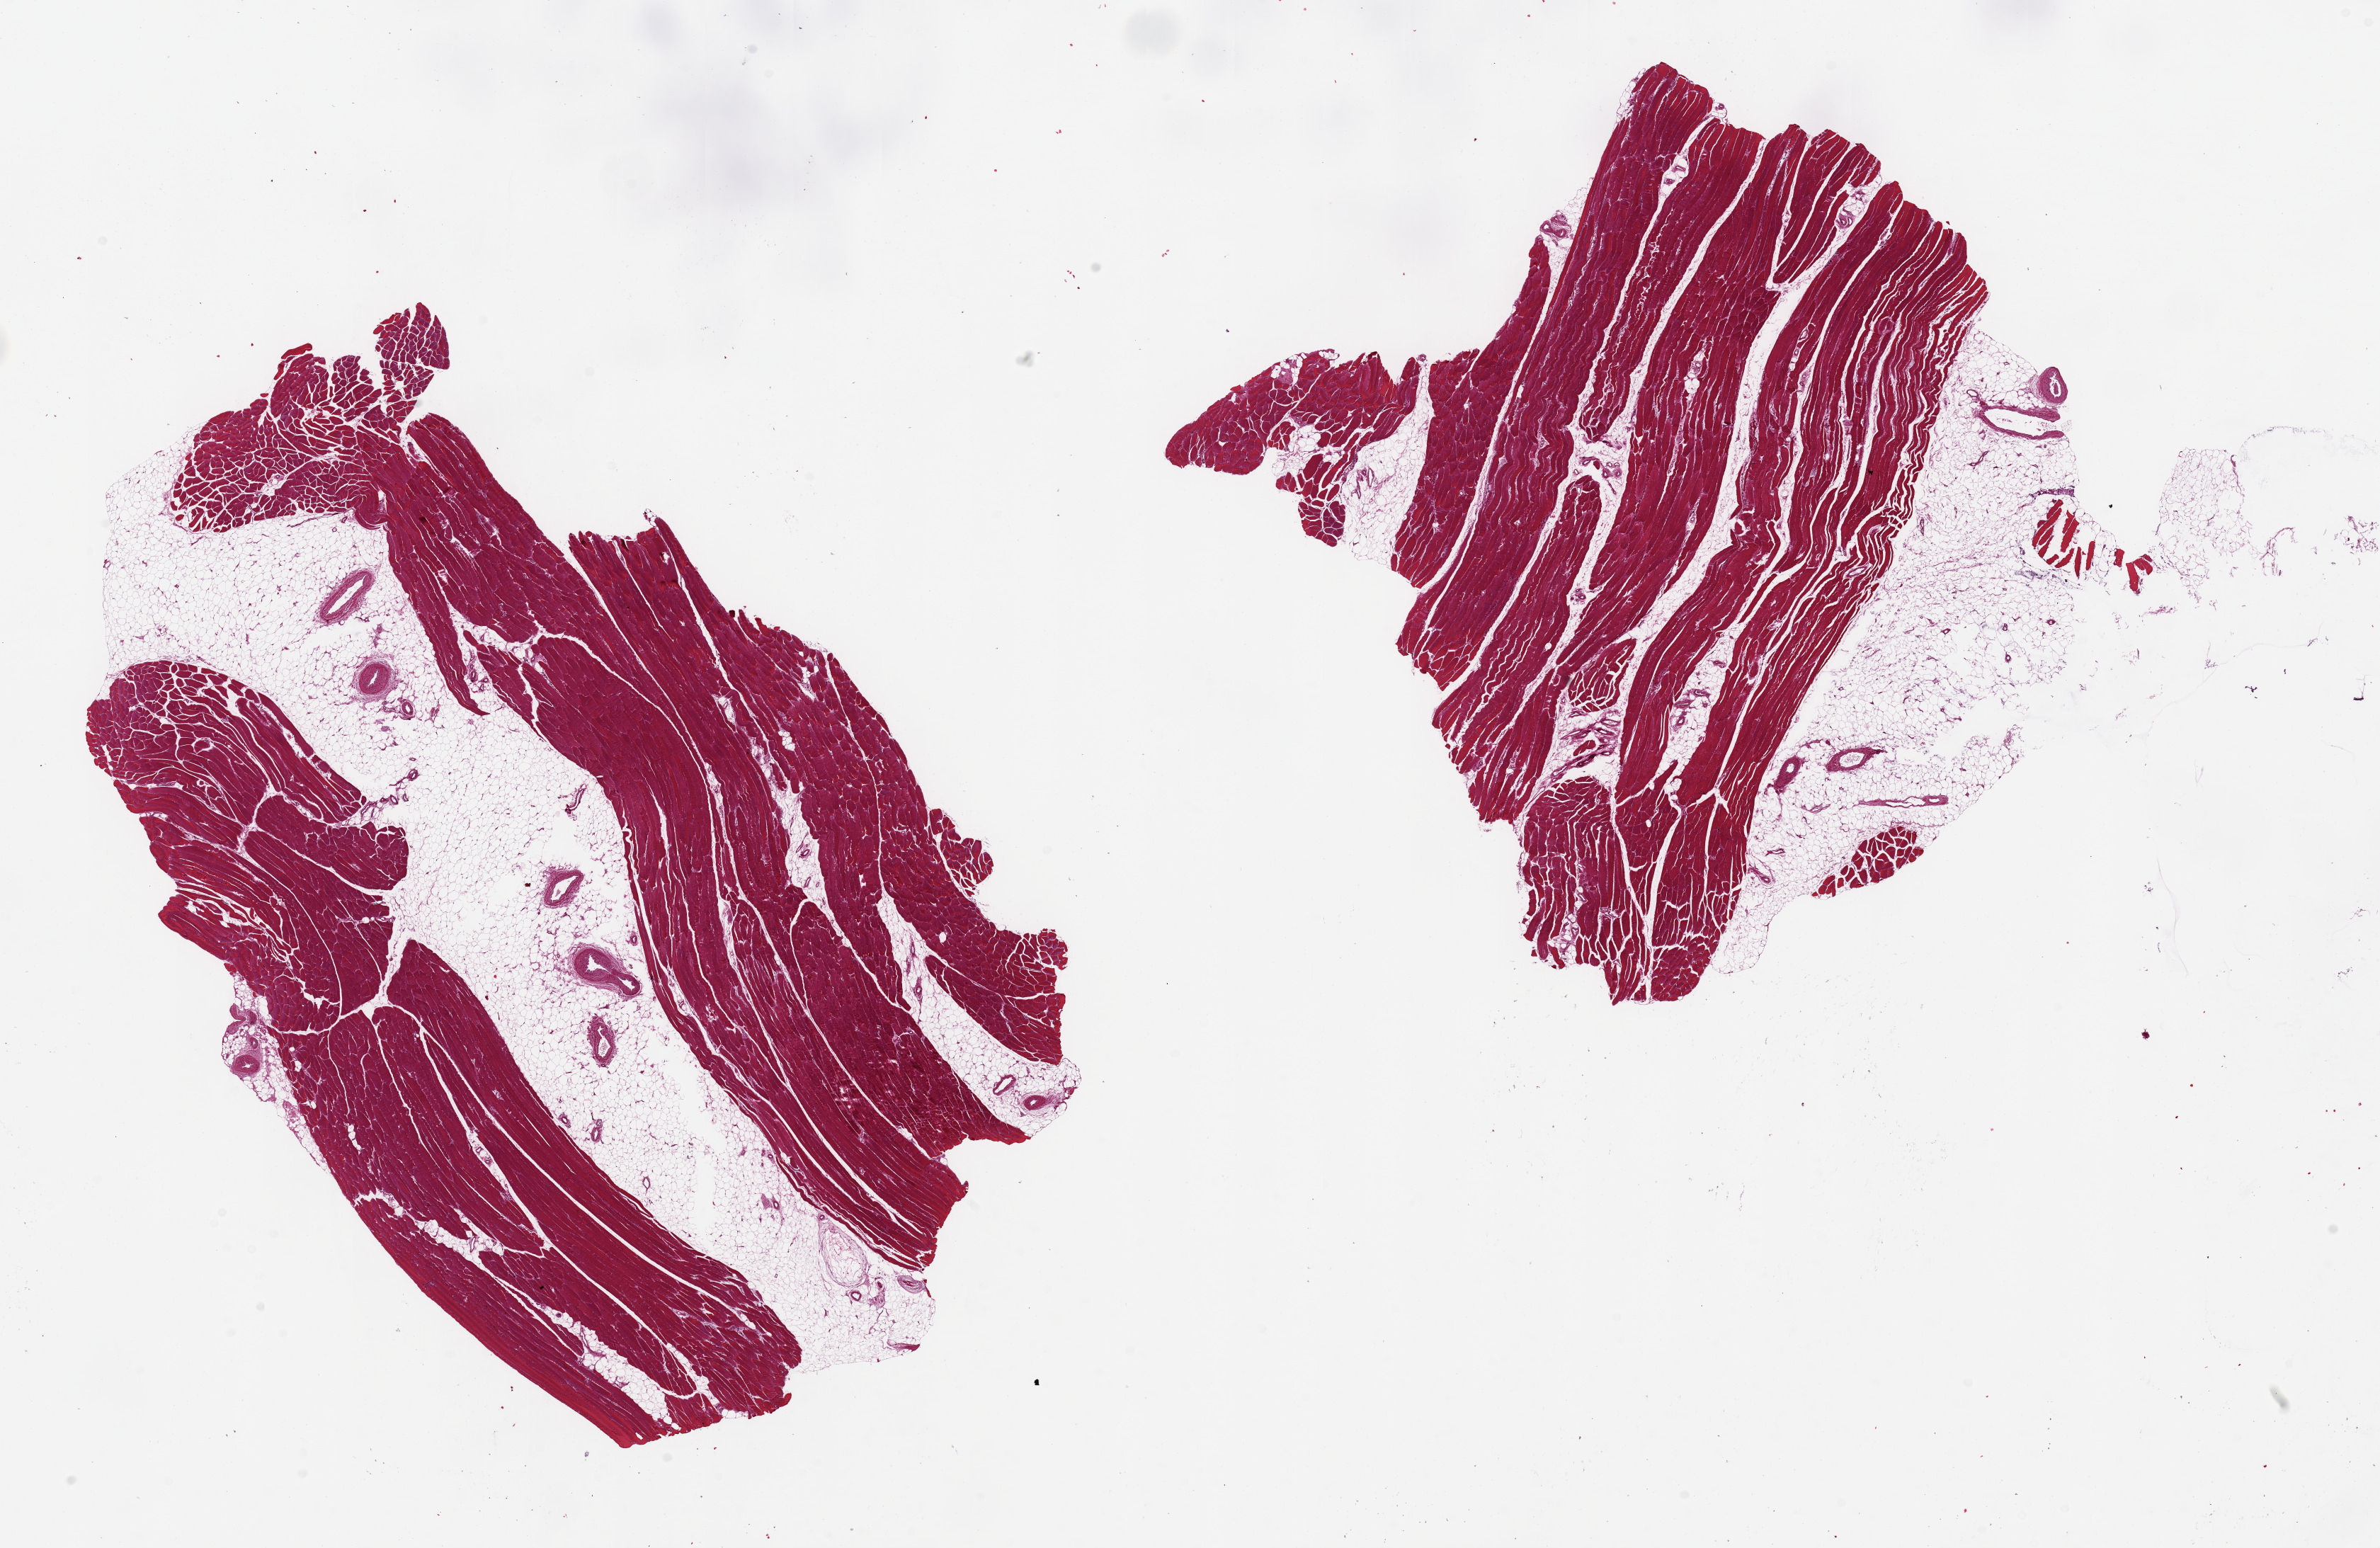
Whole-slide image, H&E stain — low-resolution overview of the scanned area, about 26.6 x 17.3 mm. PAXgene-fixed, paraffin-embedded tissue. Section of skeletal muscle (target tissue). Donor tissue sample. Donor: male.
Review note (as recorded): 2 pieces 12x8 & 9x7 mm; ~25% internal and external adipose.